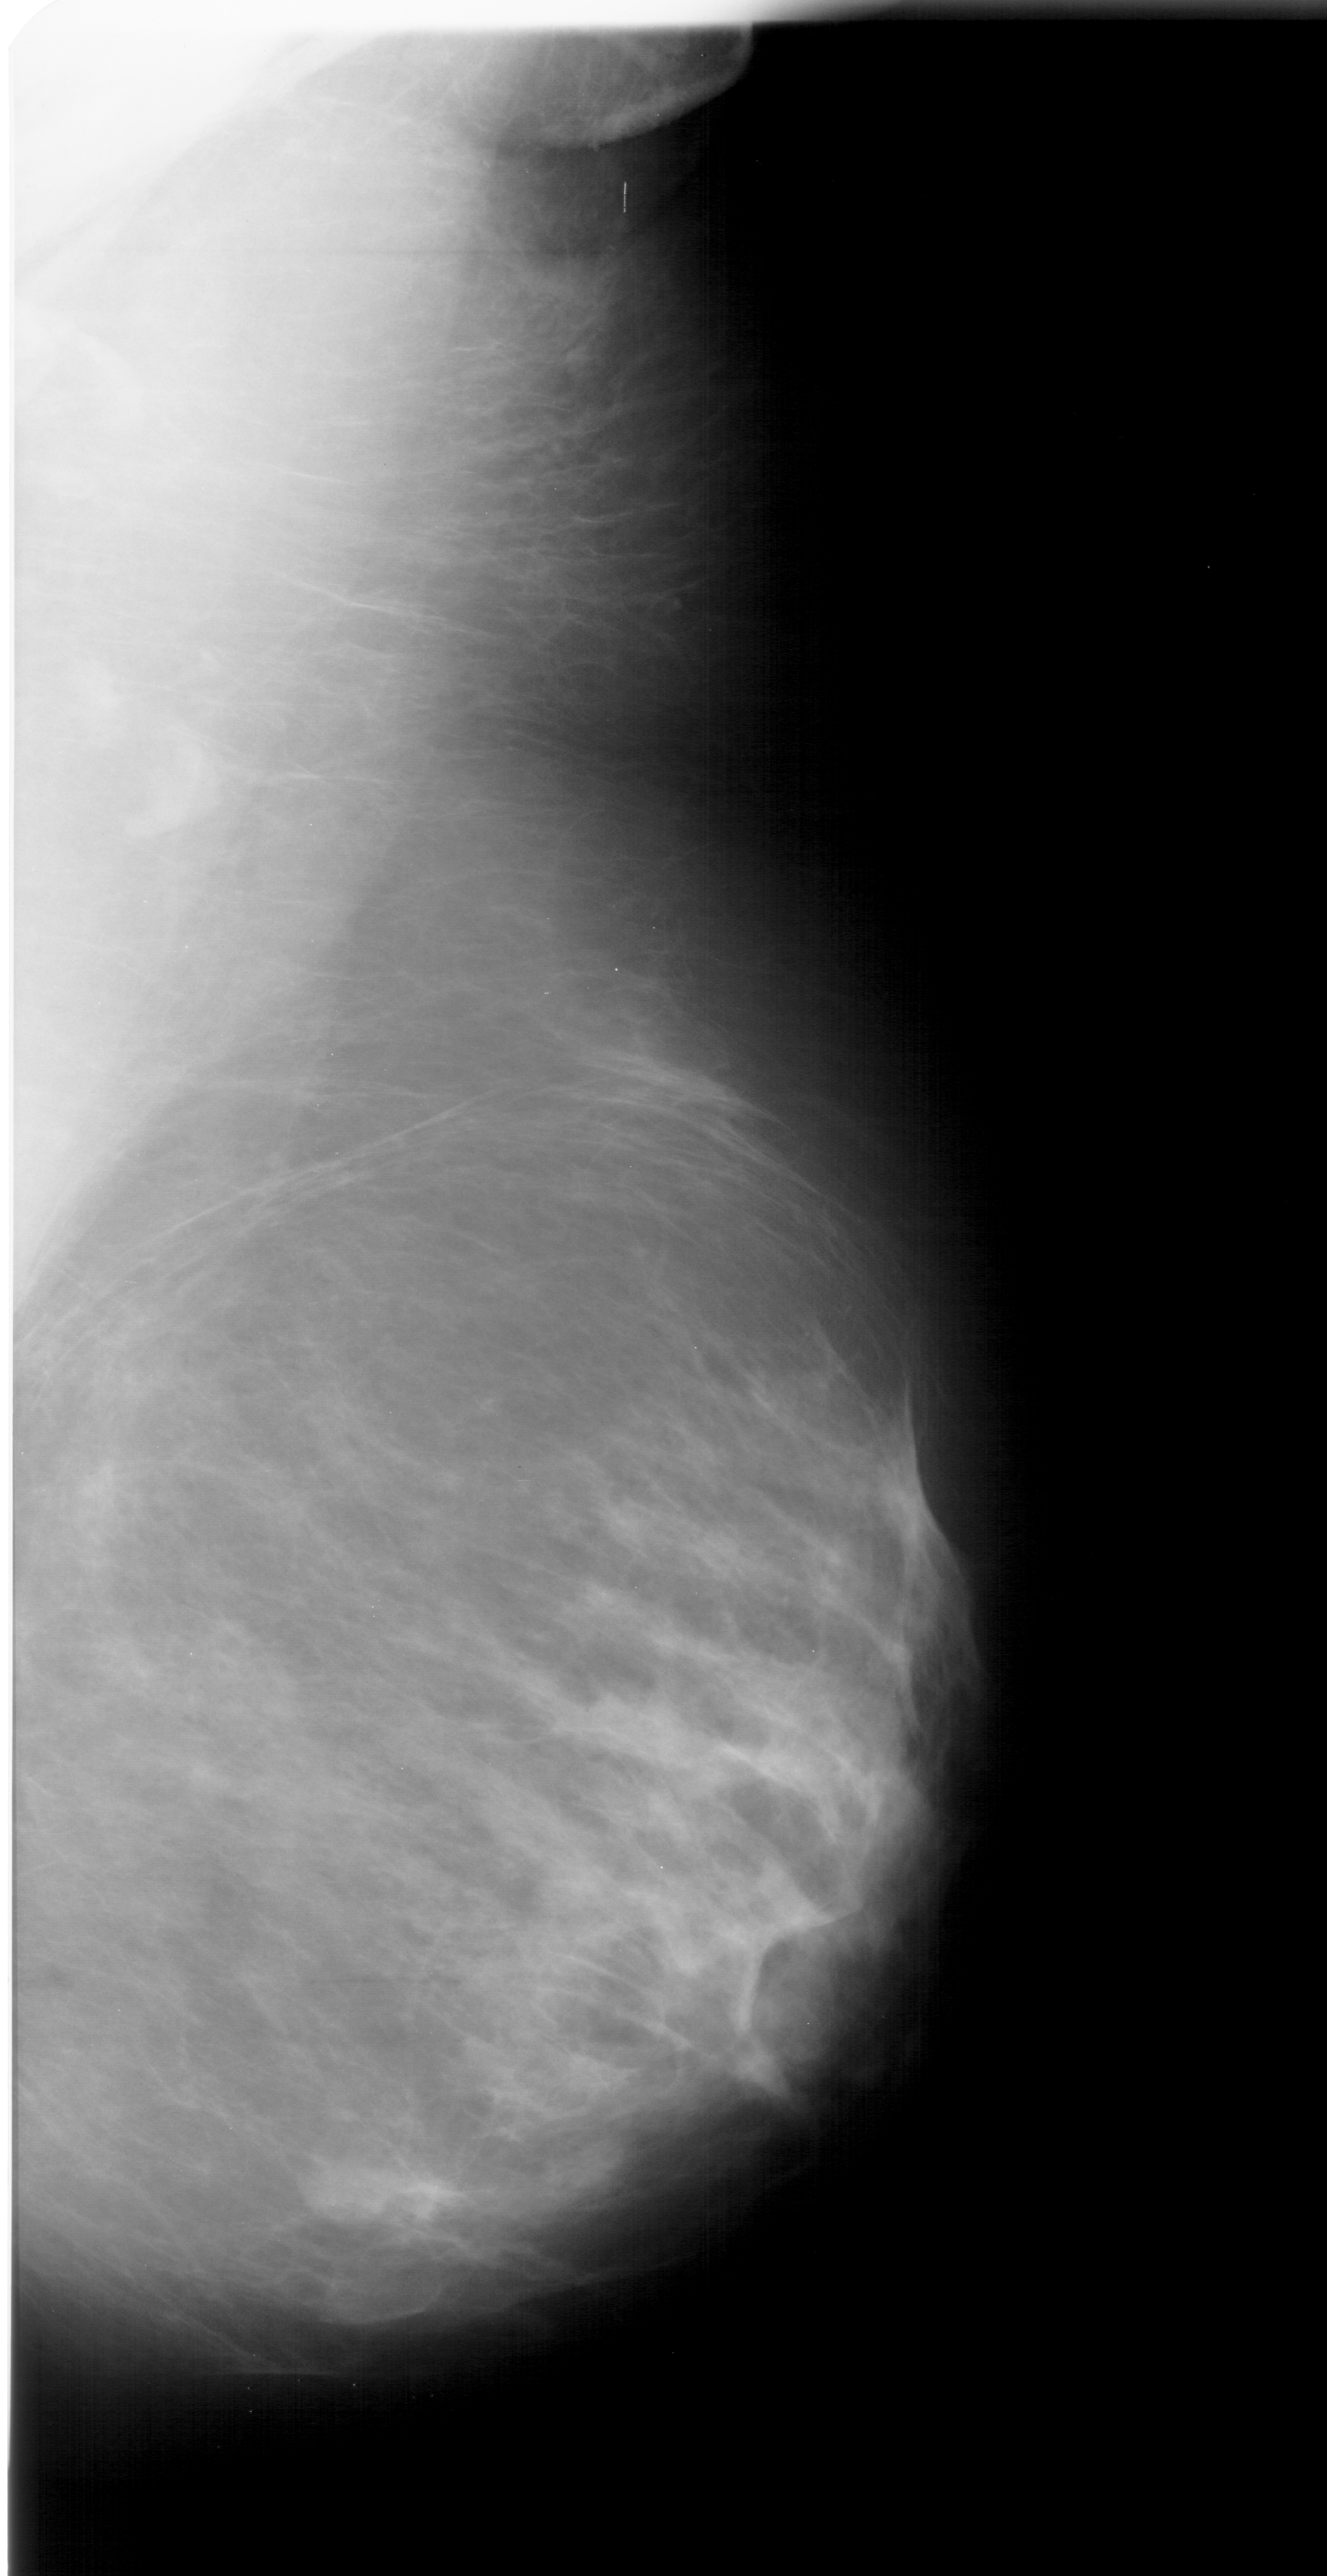
Scanned film-screen mammogram; right breast; MLO view.
Finding: mass, shape lobulated, margins circumscribed; BI-RADS assessment category 3; subtlety rating 1 on a 1 (subtle) to 5 (obvious) scale; pathology result (as recorded, not read from the image): benign.